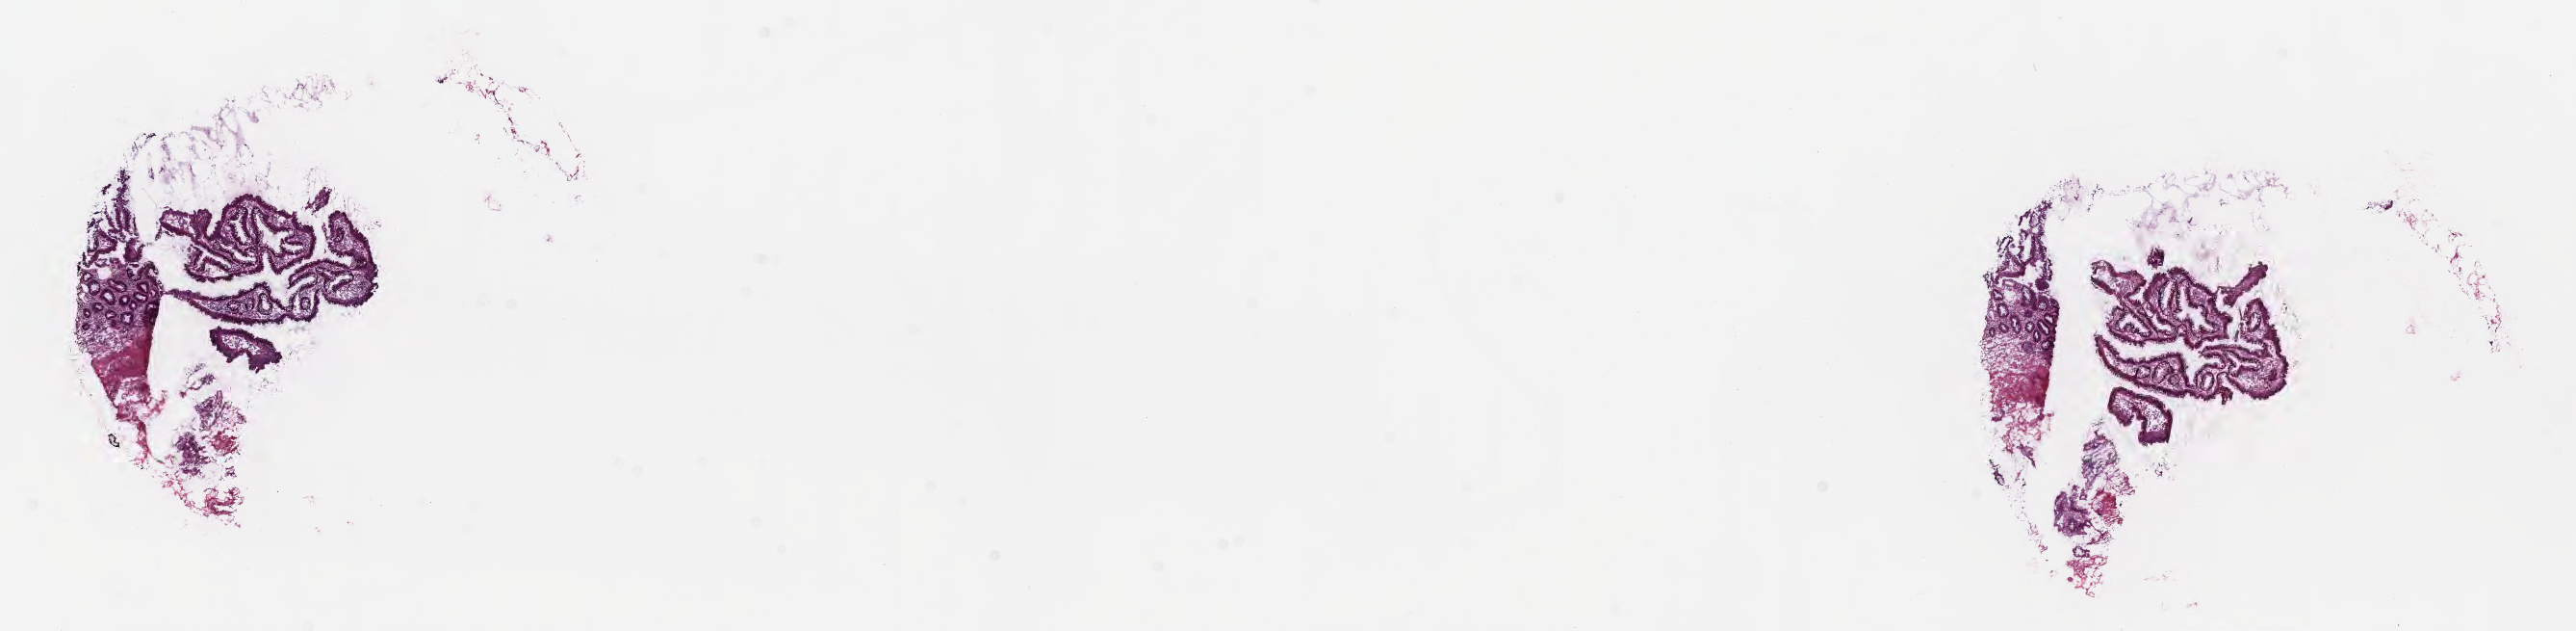
Digitized haematoxylin and eosin-stained section, shown as a low-resolution overview of the whole scanned area (about 21.6 x 5.3 mm), frozen section (tissue freezing medium), specimen: premalignant lesion from a patient with tubulovillous adenoma, NOS, anatomic site: ascending colon. Male, age 75 years at initial diagnosis. Slide review estimates, as recorded: tumor cells 80%, tumor nuclei 80%.
This section: sample classed premalignant; the patient's recorded diagnosis is given above. Section: top of the tissue portion.